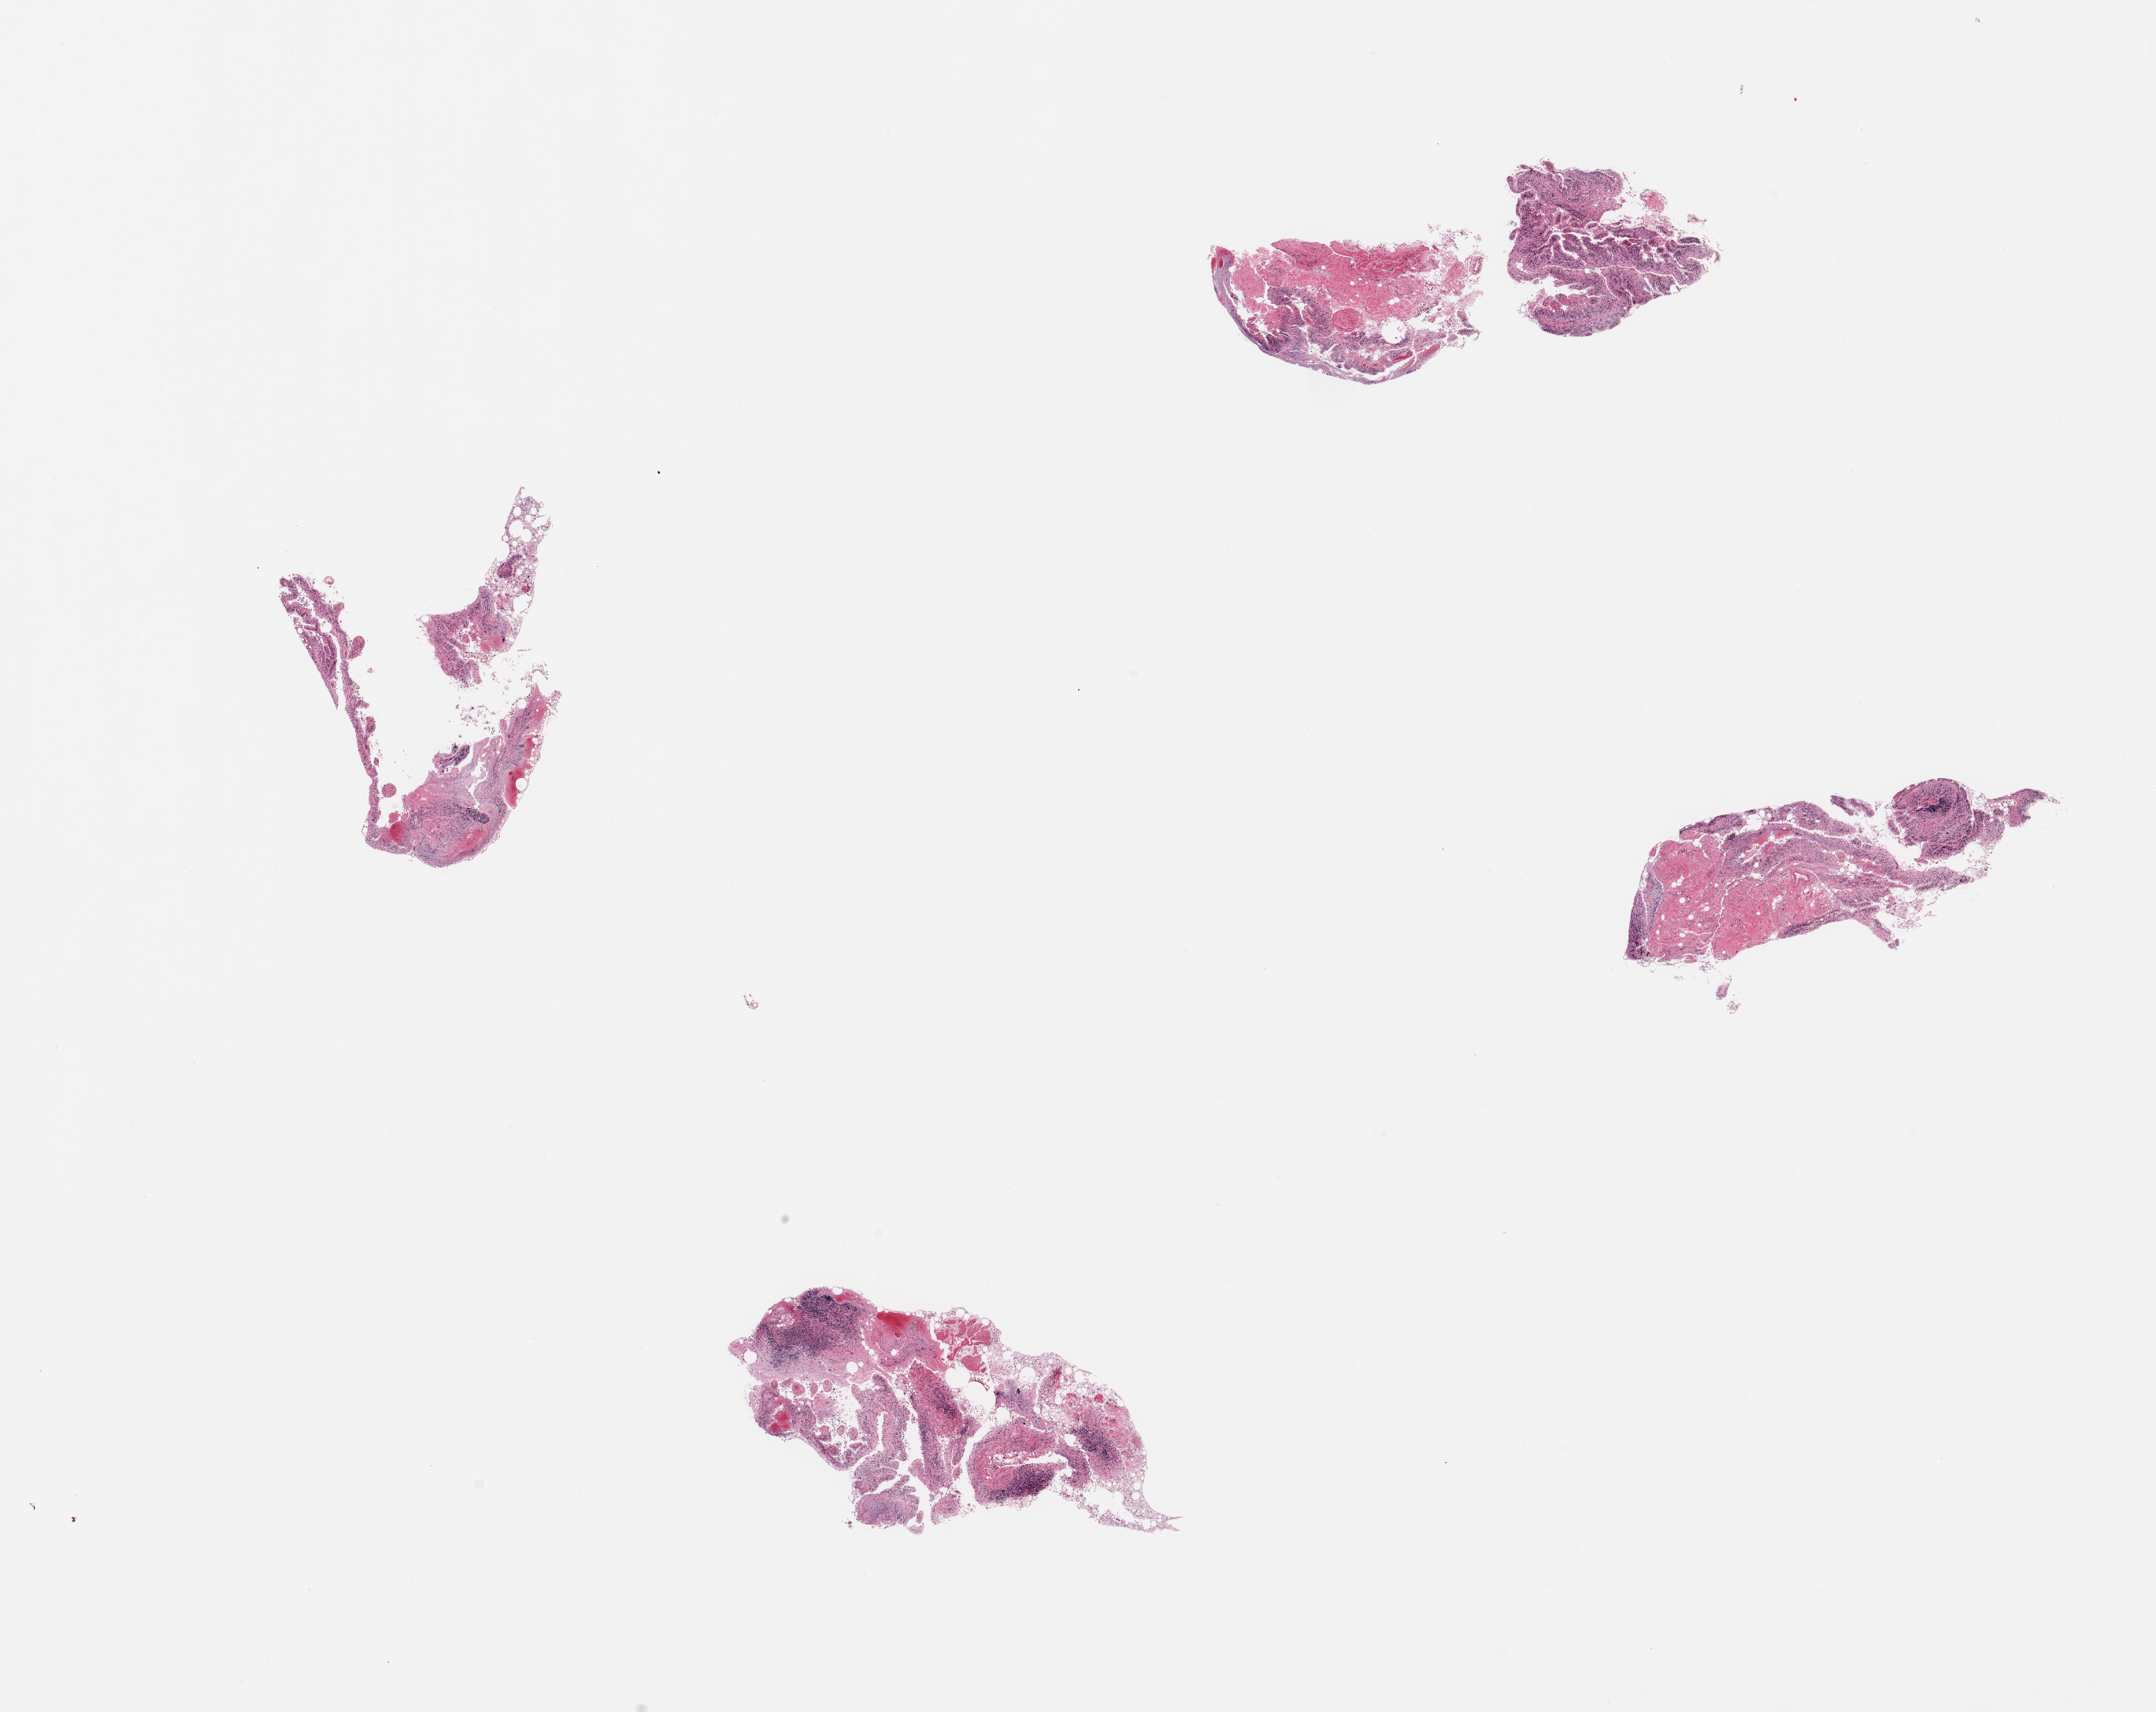
Digitized H&E-stained section — low-resolution overview of the scanned area, about 21.7 x 17.2 mm (from a 20x scan), PAXgene-fixed paraffin-embedded (PFPE) section, target tissue: ileum, donor tissue sample. Male donor.
Pathologist's review note for this sample: 4 pieces, only trace target lymphoid aggregates in mucosa with advanced autolysis.